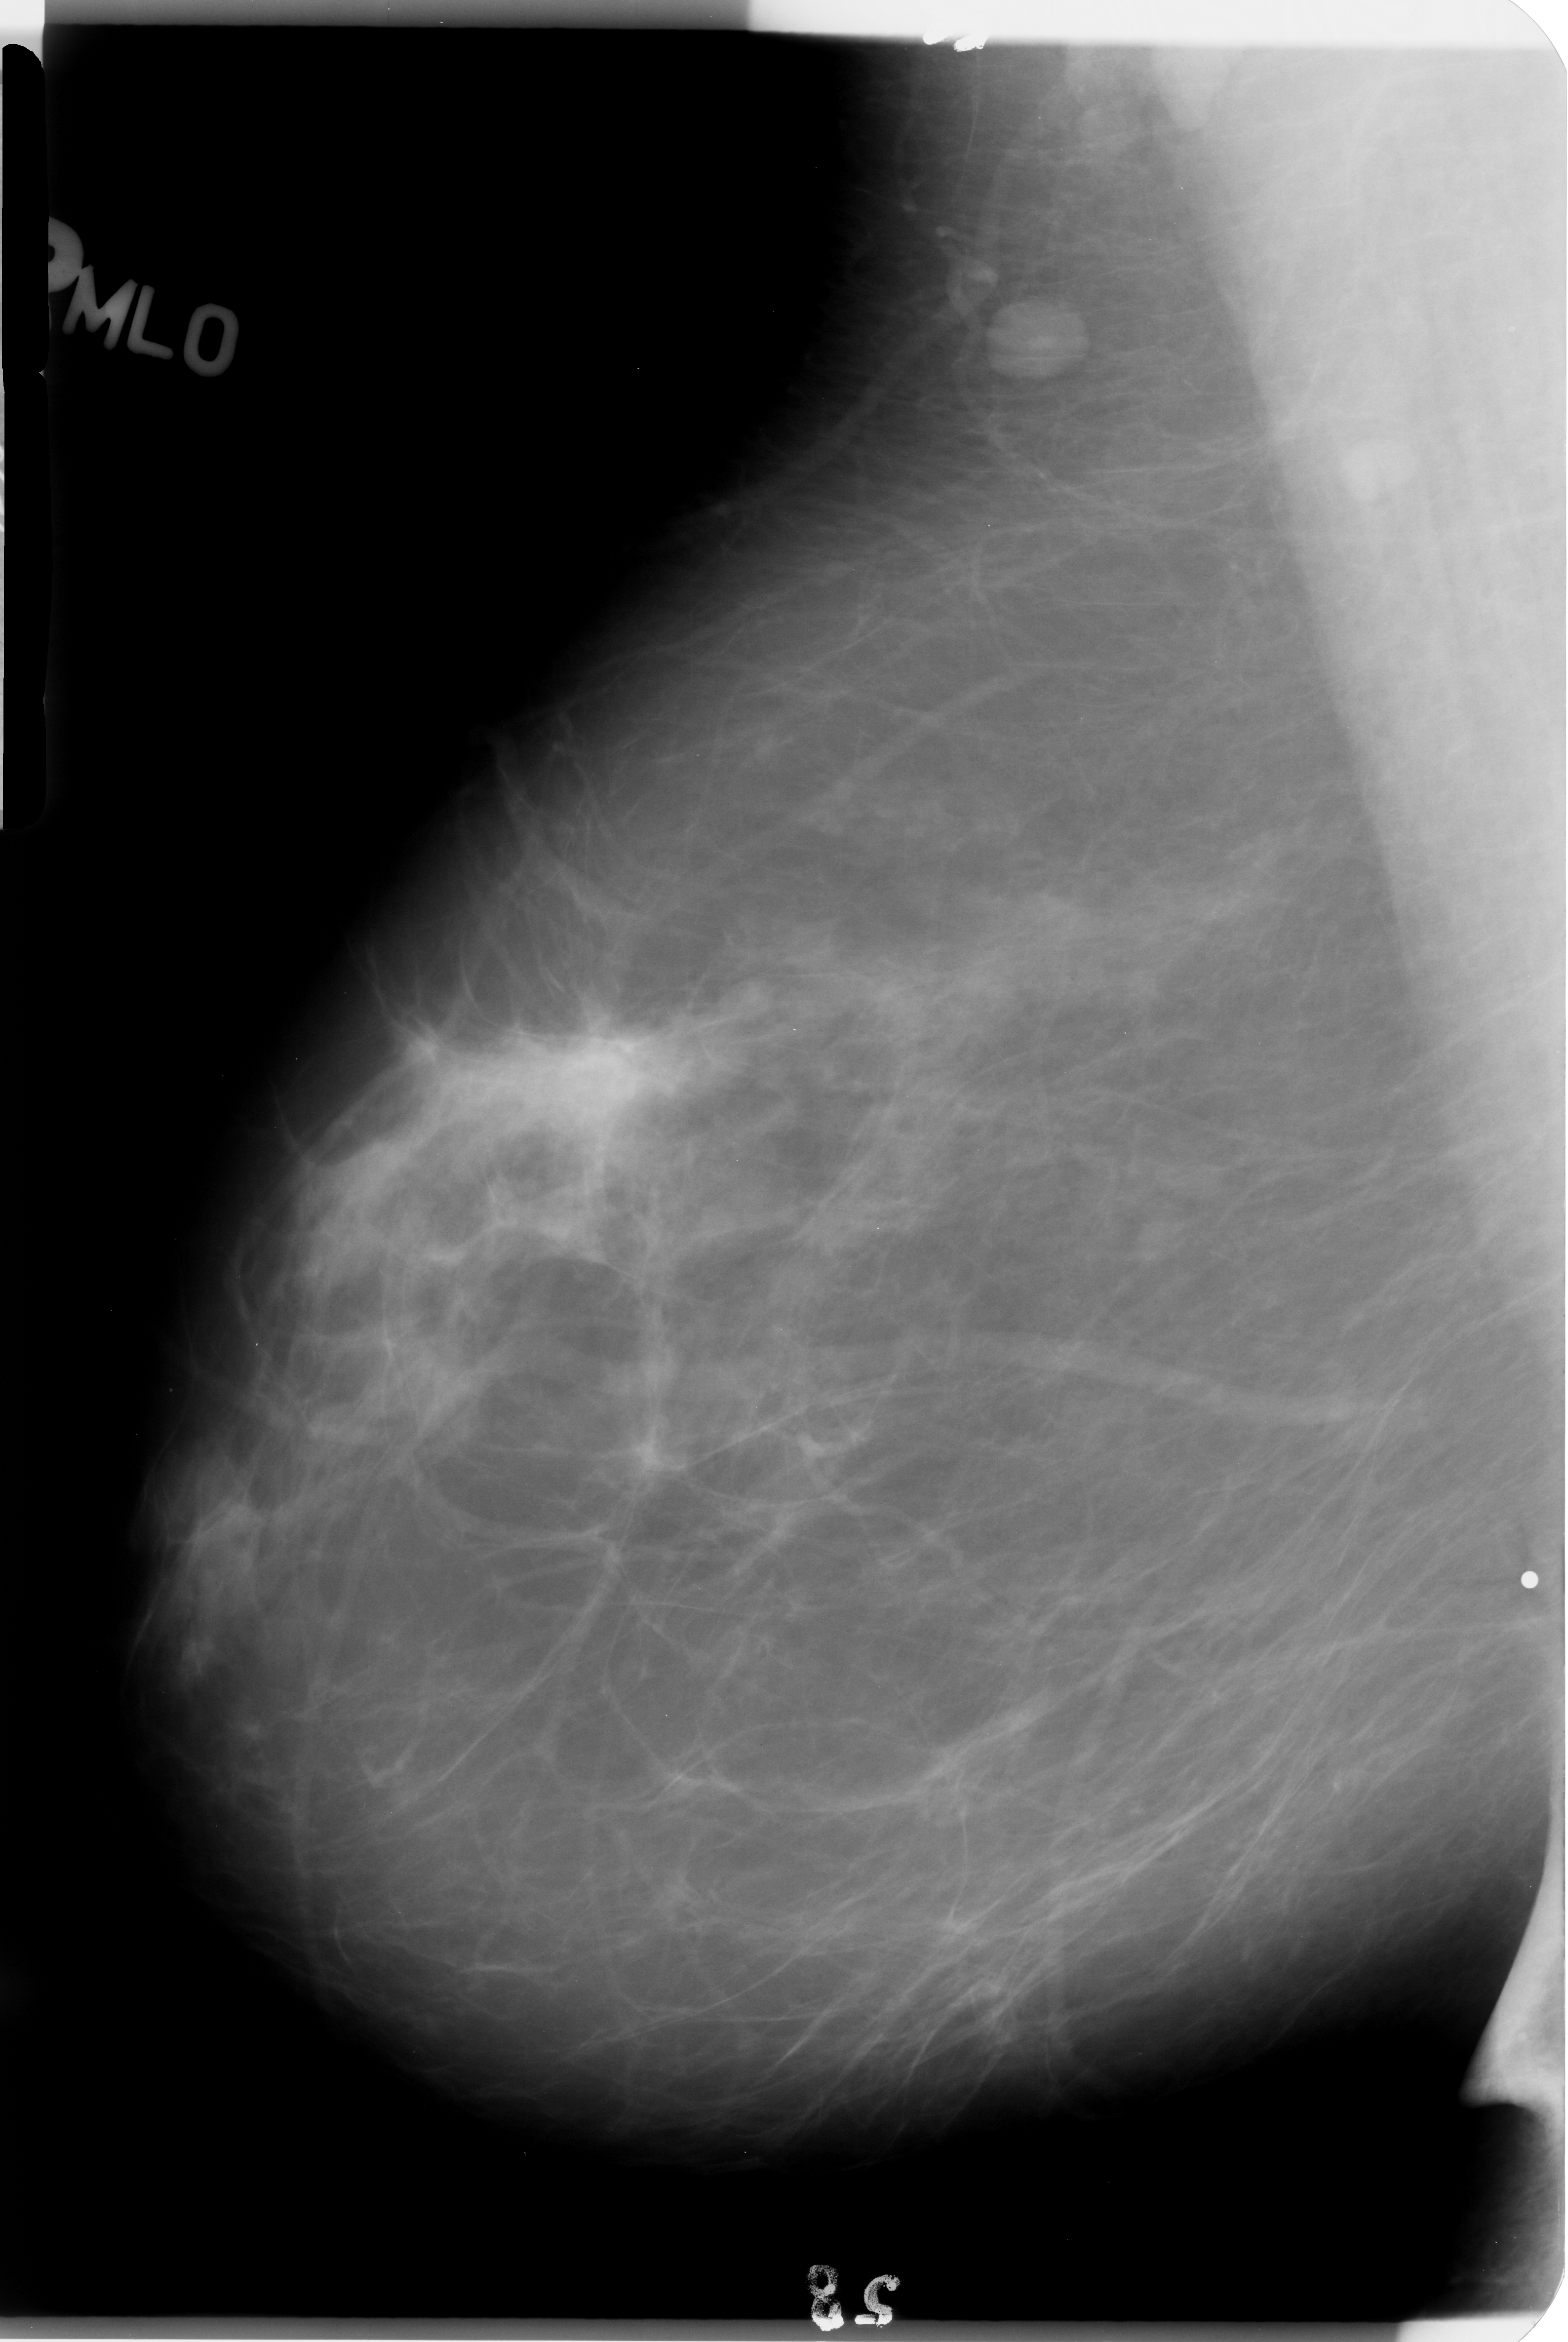
Mammogram (digitized film); right breast; MLO view; breast composition: scattered fibroglandular densities (BI-RADS density category 2 of 4).
- Radiologist-marked abnormalities on this image: mass, shape irregular, margins ill defined; BI-RADS assessment category 4; subtlety rating 2 on a 1 (subtle) to 5 (obvious) scale; pathology result (as recorded, not read from the image): benign.